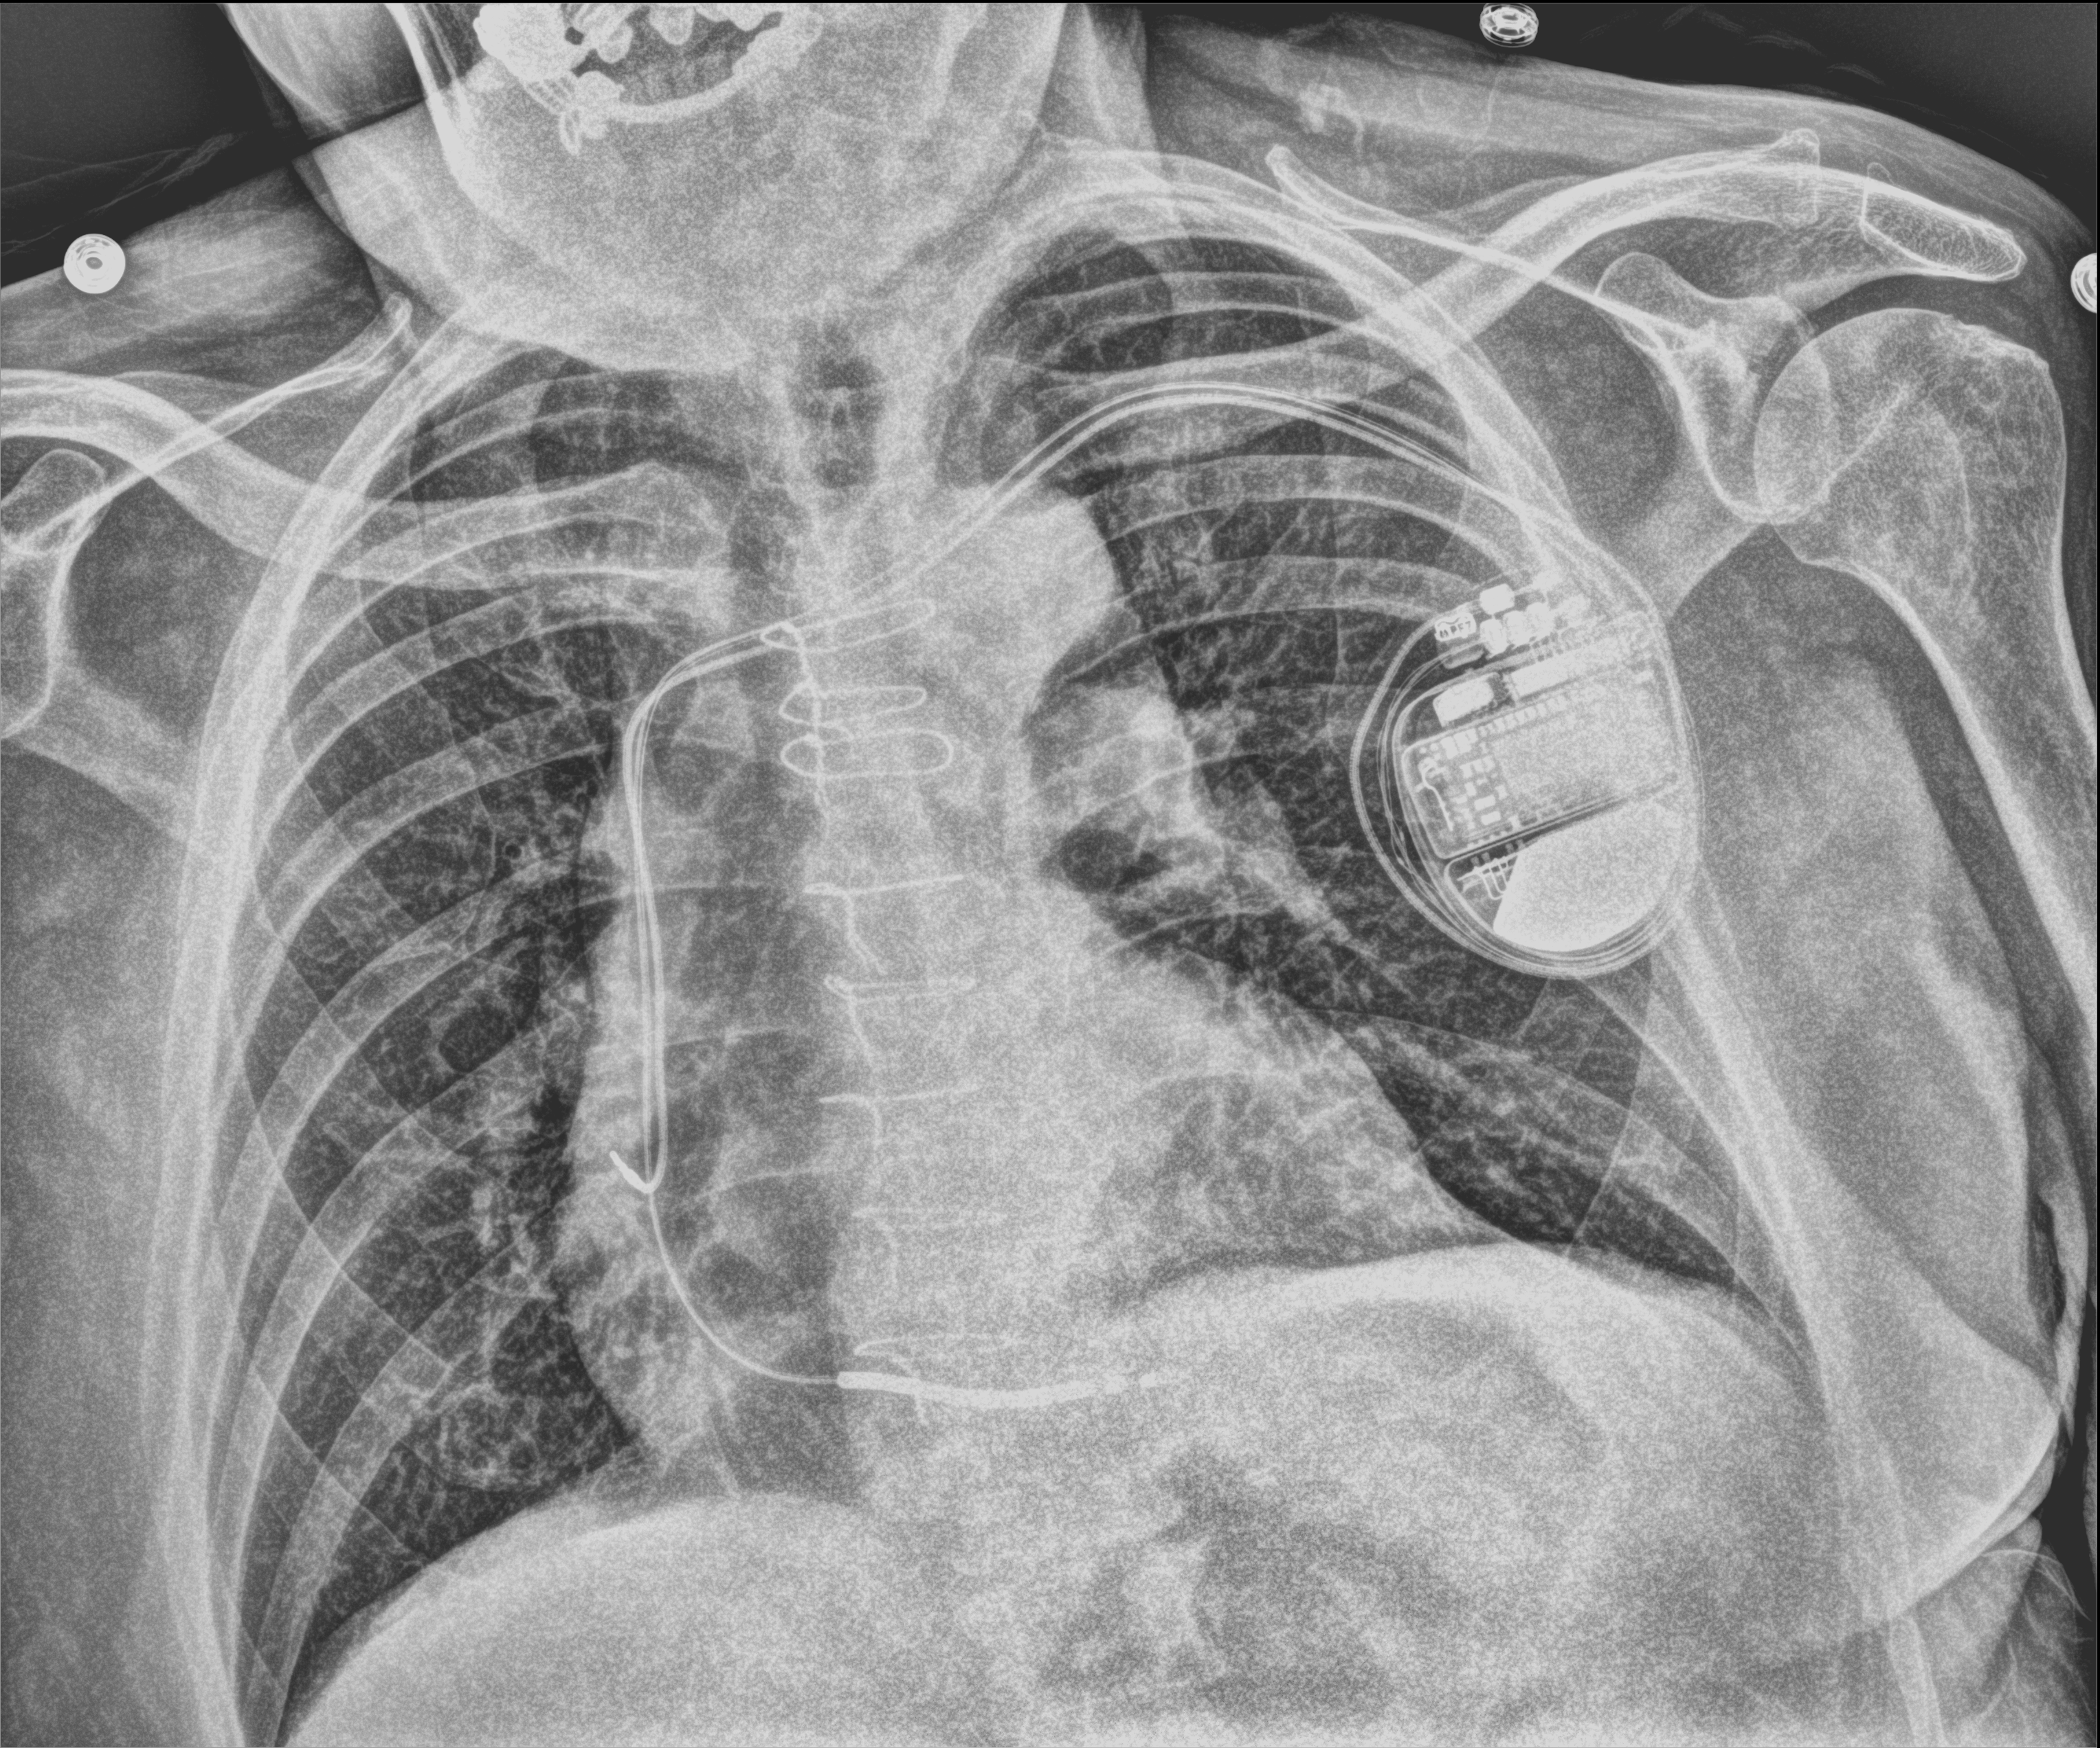
Chest X-ray (portable), anteroposterior (AP) projection. Male patient hospitalised with COVID-19, age 75–90 years.
Hospital-stay facts (about this admission, not read from this image; timing relative to this image not recorded): admitted to intensive care during this hospital stay: yes; mechanically ventilated during this hospital stay: yes.